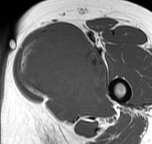
MRI of an extremity soft-tissue mass, one axial slice; MR volume resampled by the dataset authors to the PET/CT grid (not the native acquisition matrix); 152 × 144 image matrix, field of view 148 × 141 mm. Female patient. From the clinical record (not read from this slice): histological type: pleiomorphic leiomyosarcoma; grade: intermediate; site of the primary tumour: left thigh.
Structures marked on this image (expert contour drawn on MRI and transferred to this co-registered scan by the dataset authors):
- gross tumour volume including surrounding oedema: bounding box <18,35,105,104> (left, top, right, bottom; pixels)
- gross tumour volume (mass): <18,35,105,102>